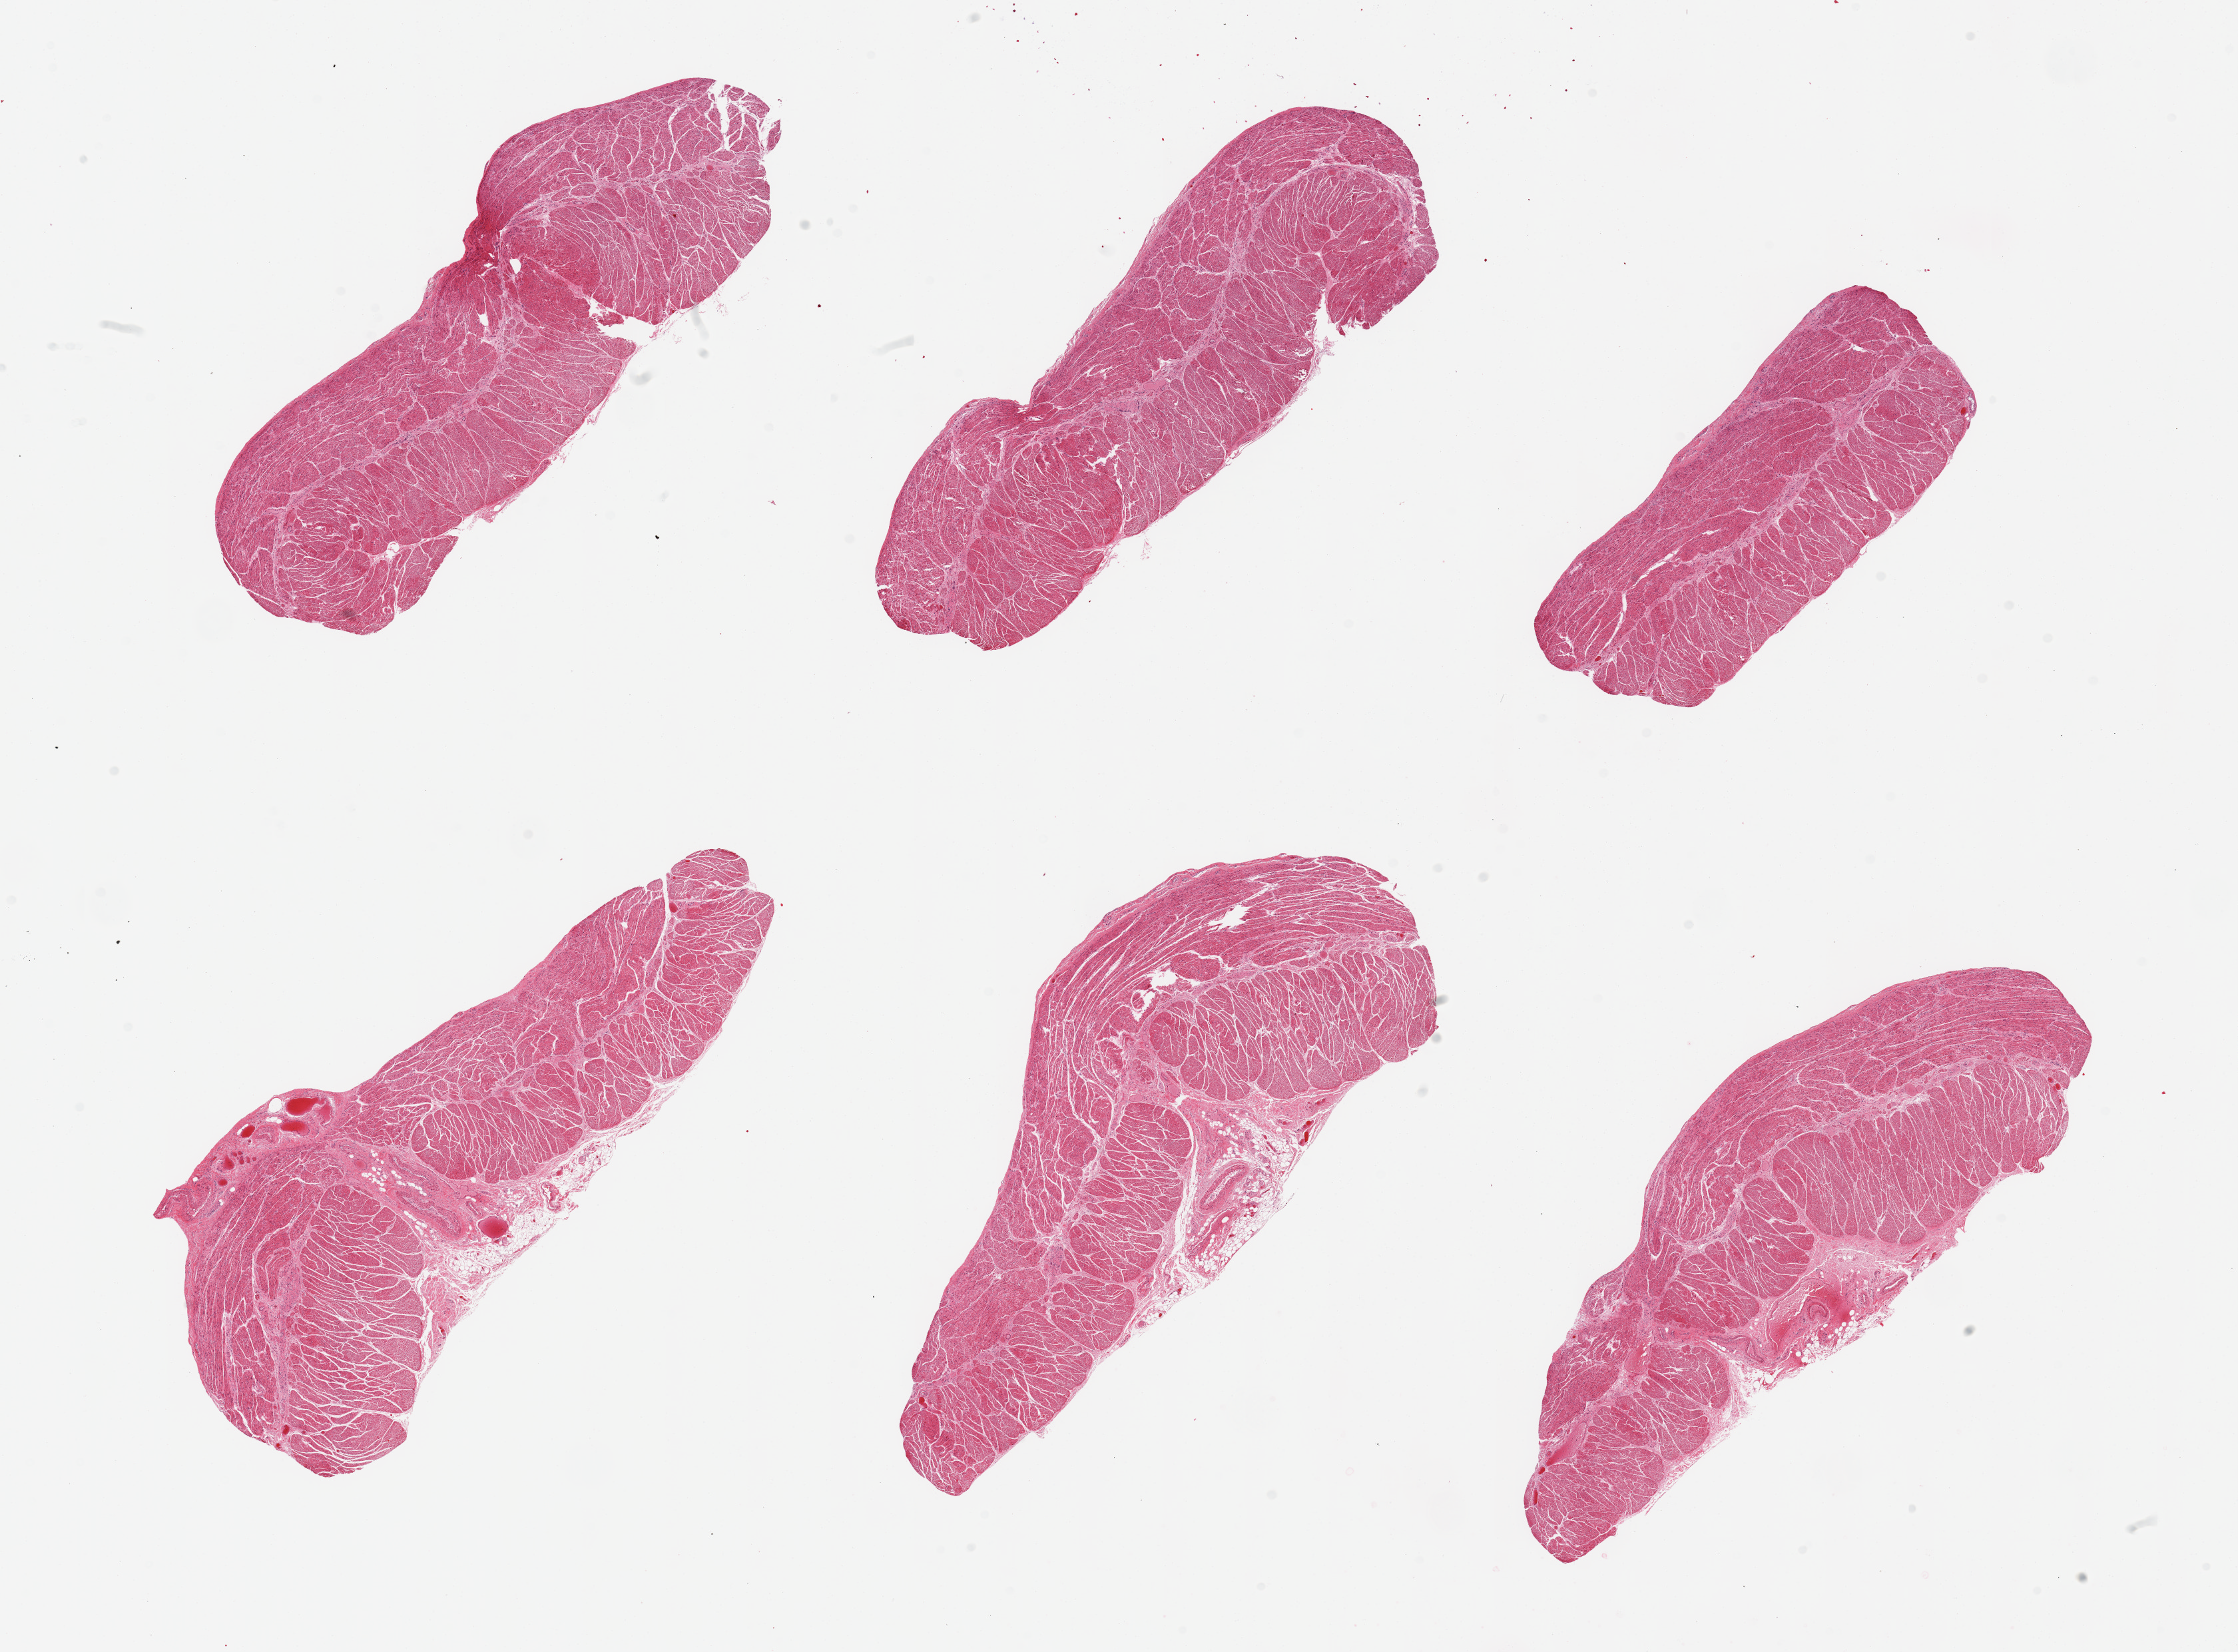
Digitized hematoxylin and eosin (H&E)-stained section — low-resolution overview of the scanned area, about 26.6 x 19.6 mm; PAXgene-fixed, paraffin-embedded tissue; sampled site (target tissue): gastroesophageal junction; donor tissue sample. Donor: male.
• review note (as recorded): 6 pieces; well trimmed